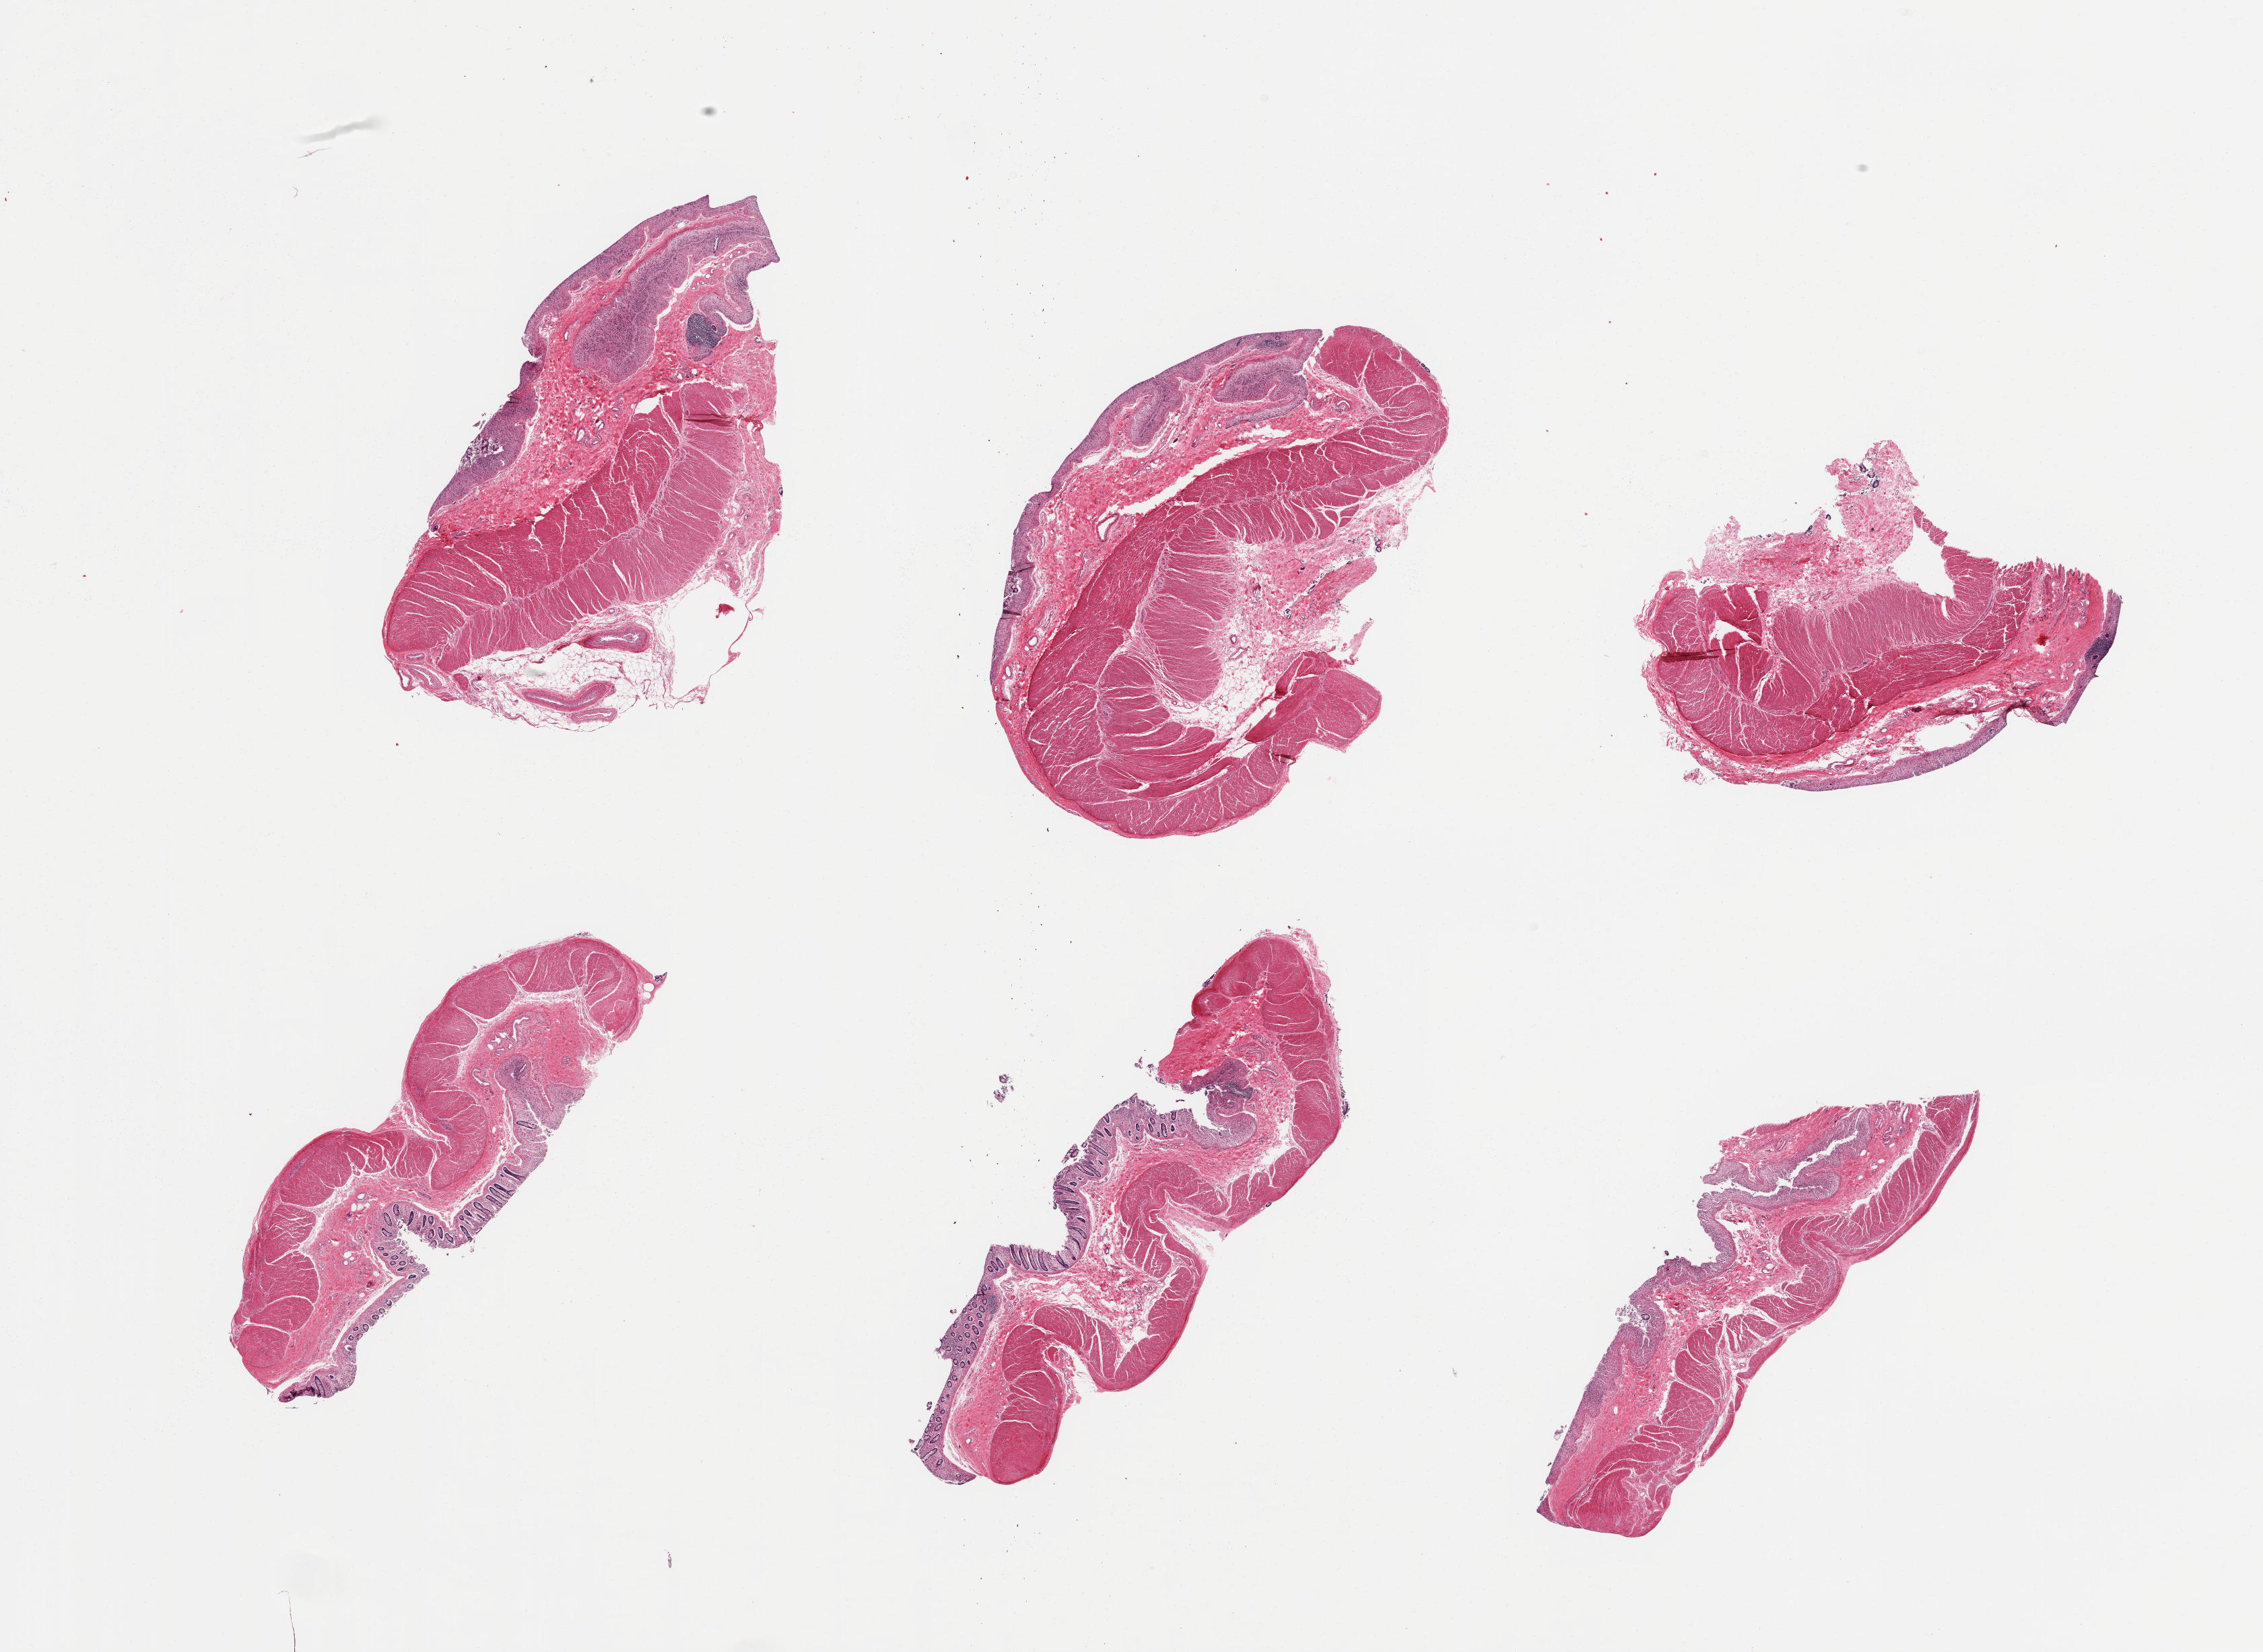
H&E whole-slide image — a low-resolution overview of the entire scanned area, about 26.6 x 19.4 mm; PAXgene-fixed, paraffin-embedded tissue; sampled site (target tissue): transverse colon; donor tissue sample. Donor: female.
Review note (as recorded): 6 pieces; full thickness colon, mild melanosis, mucosa more autolyzed than muscularis.